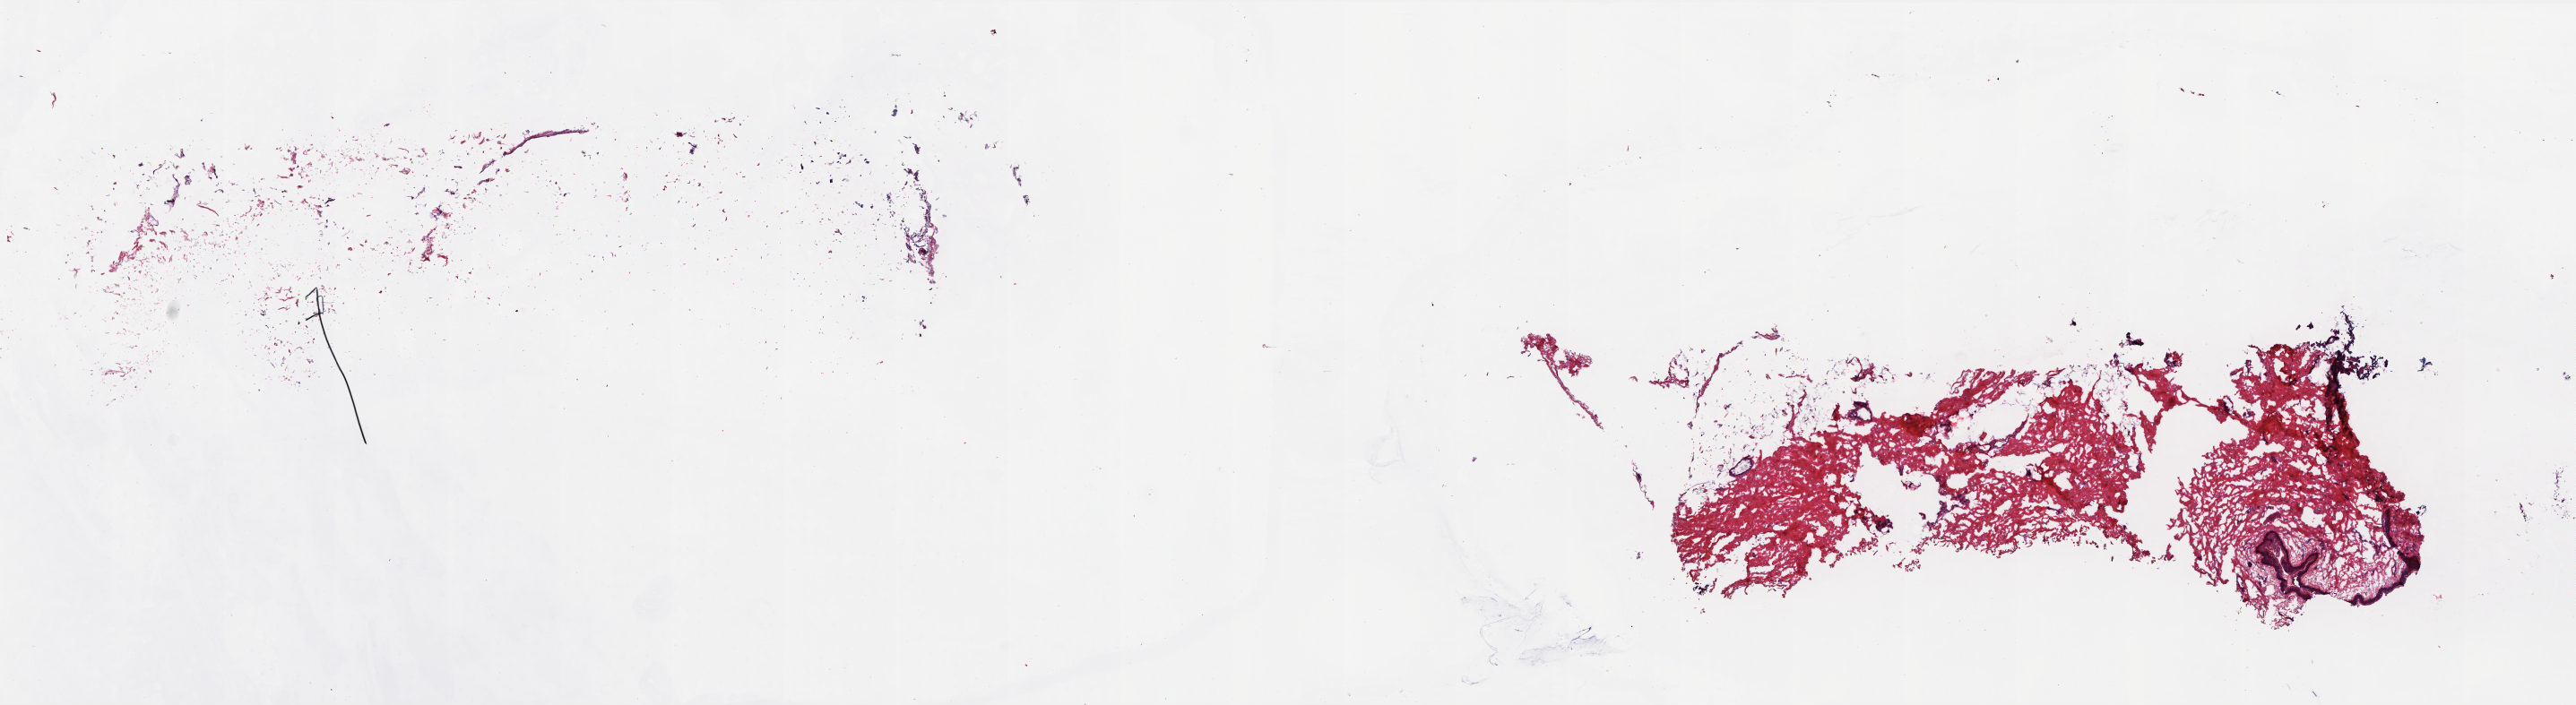
H&E-stained whole-slide image — whole scanned area (about 23.0 x 6.3 mm, acquisition: 20x scan) shown as a low-resolution overview; frozen section from the top of the tissue portion; sample: solid tissue normal (non-tumour tissue), connective, subcutaneous and other soft tissues. Female, age 82 years at initial diagnosis. Pathologist review of this section (percent, as recorded): tumour cells 0%, tumour nuclei 0%, normal cells 100%, stromal cells 0%, necrosis 0%. Inflammatory infiltration, as recorded: lymphocyte infiltration 1%, monocyte infiltration 0%, neutrophil infiltration 0%.
This section: solid tissue normal (non-tumour) sample from the same patient. Patient diagnosis: Leiomyosarcoma, NOS.